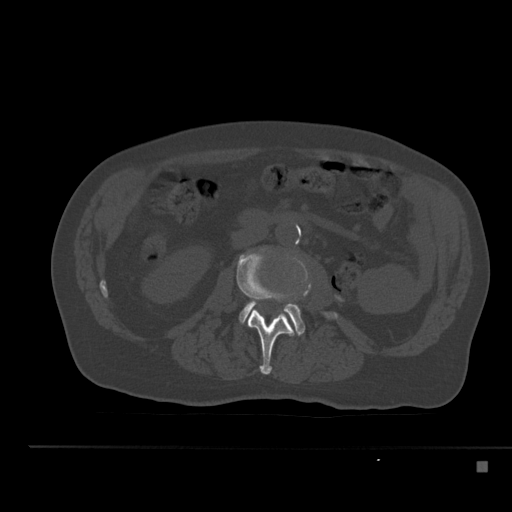
CT including the spine, one axial slice; slice 177 of 517 in the series (ordered by position); reconstruction kernel Br40s; 120 kVp; bone window (W 1800 / L 400 HU); 512 × 512 image matrix, field of view 408 × 408 mm. Male patient, age 70 years. Case-level facts recorded for this patient, not image findings: primary cancer: renal.
Structures marked on this image (semi-automatically segmented with operator editing):
- L2 vertebra: bounding box <237,249,295,375> (left, top, right, bottom; pixels)
- L3 vertebra: <239,284,337,335>